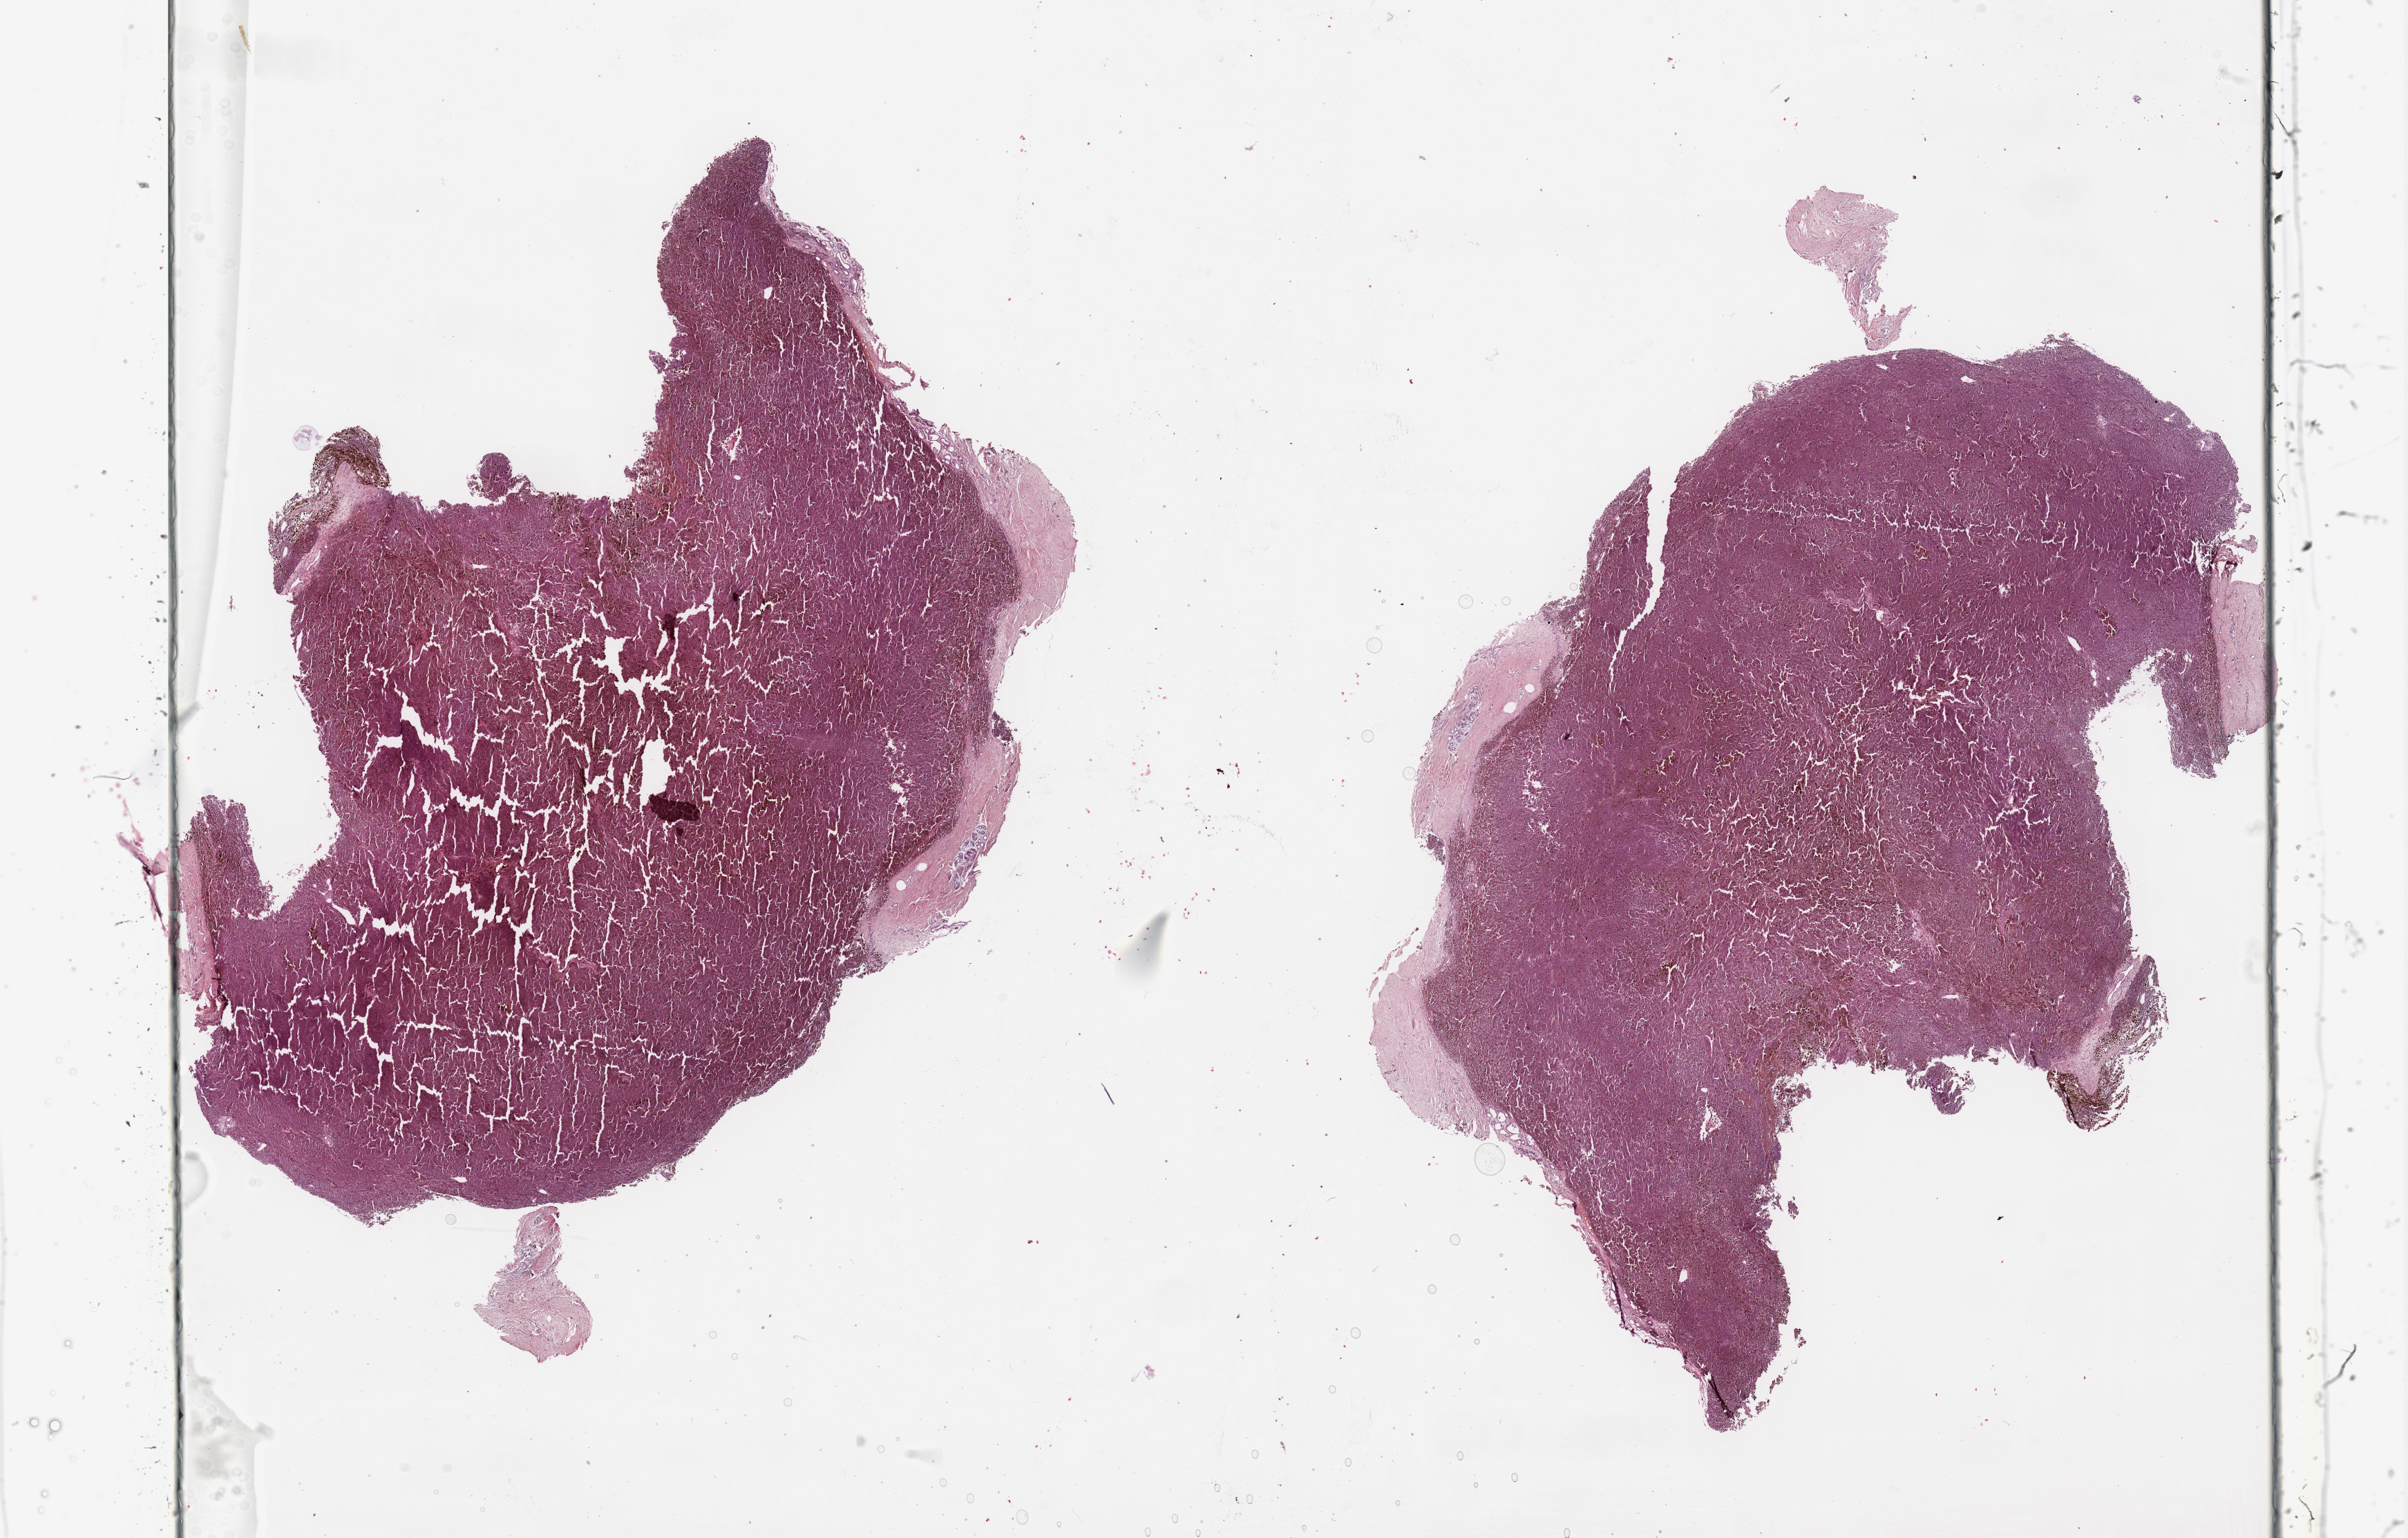
Digitized Hematoxylin and eosin (H&E) stained tissue section (whole slide) — low-resolution overview of the scanned area, about 27.6 x 17.6 mm (acquisition: 20x scan), tumour tissue sample, sampled site: trunk. Female, 54 y/o. Composition of this section per pathologist review: tumour nuclei 95%, necrosis 0%.
This section: metastatic tumour tissue. Patient diagnosis: Malignant melanoma, NOS.